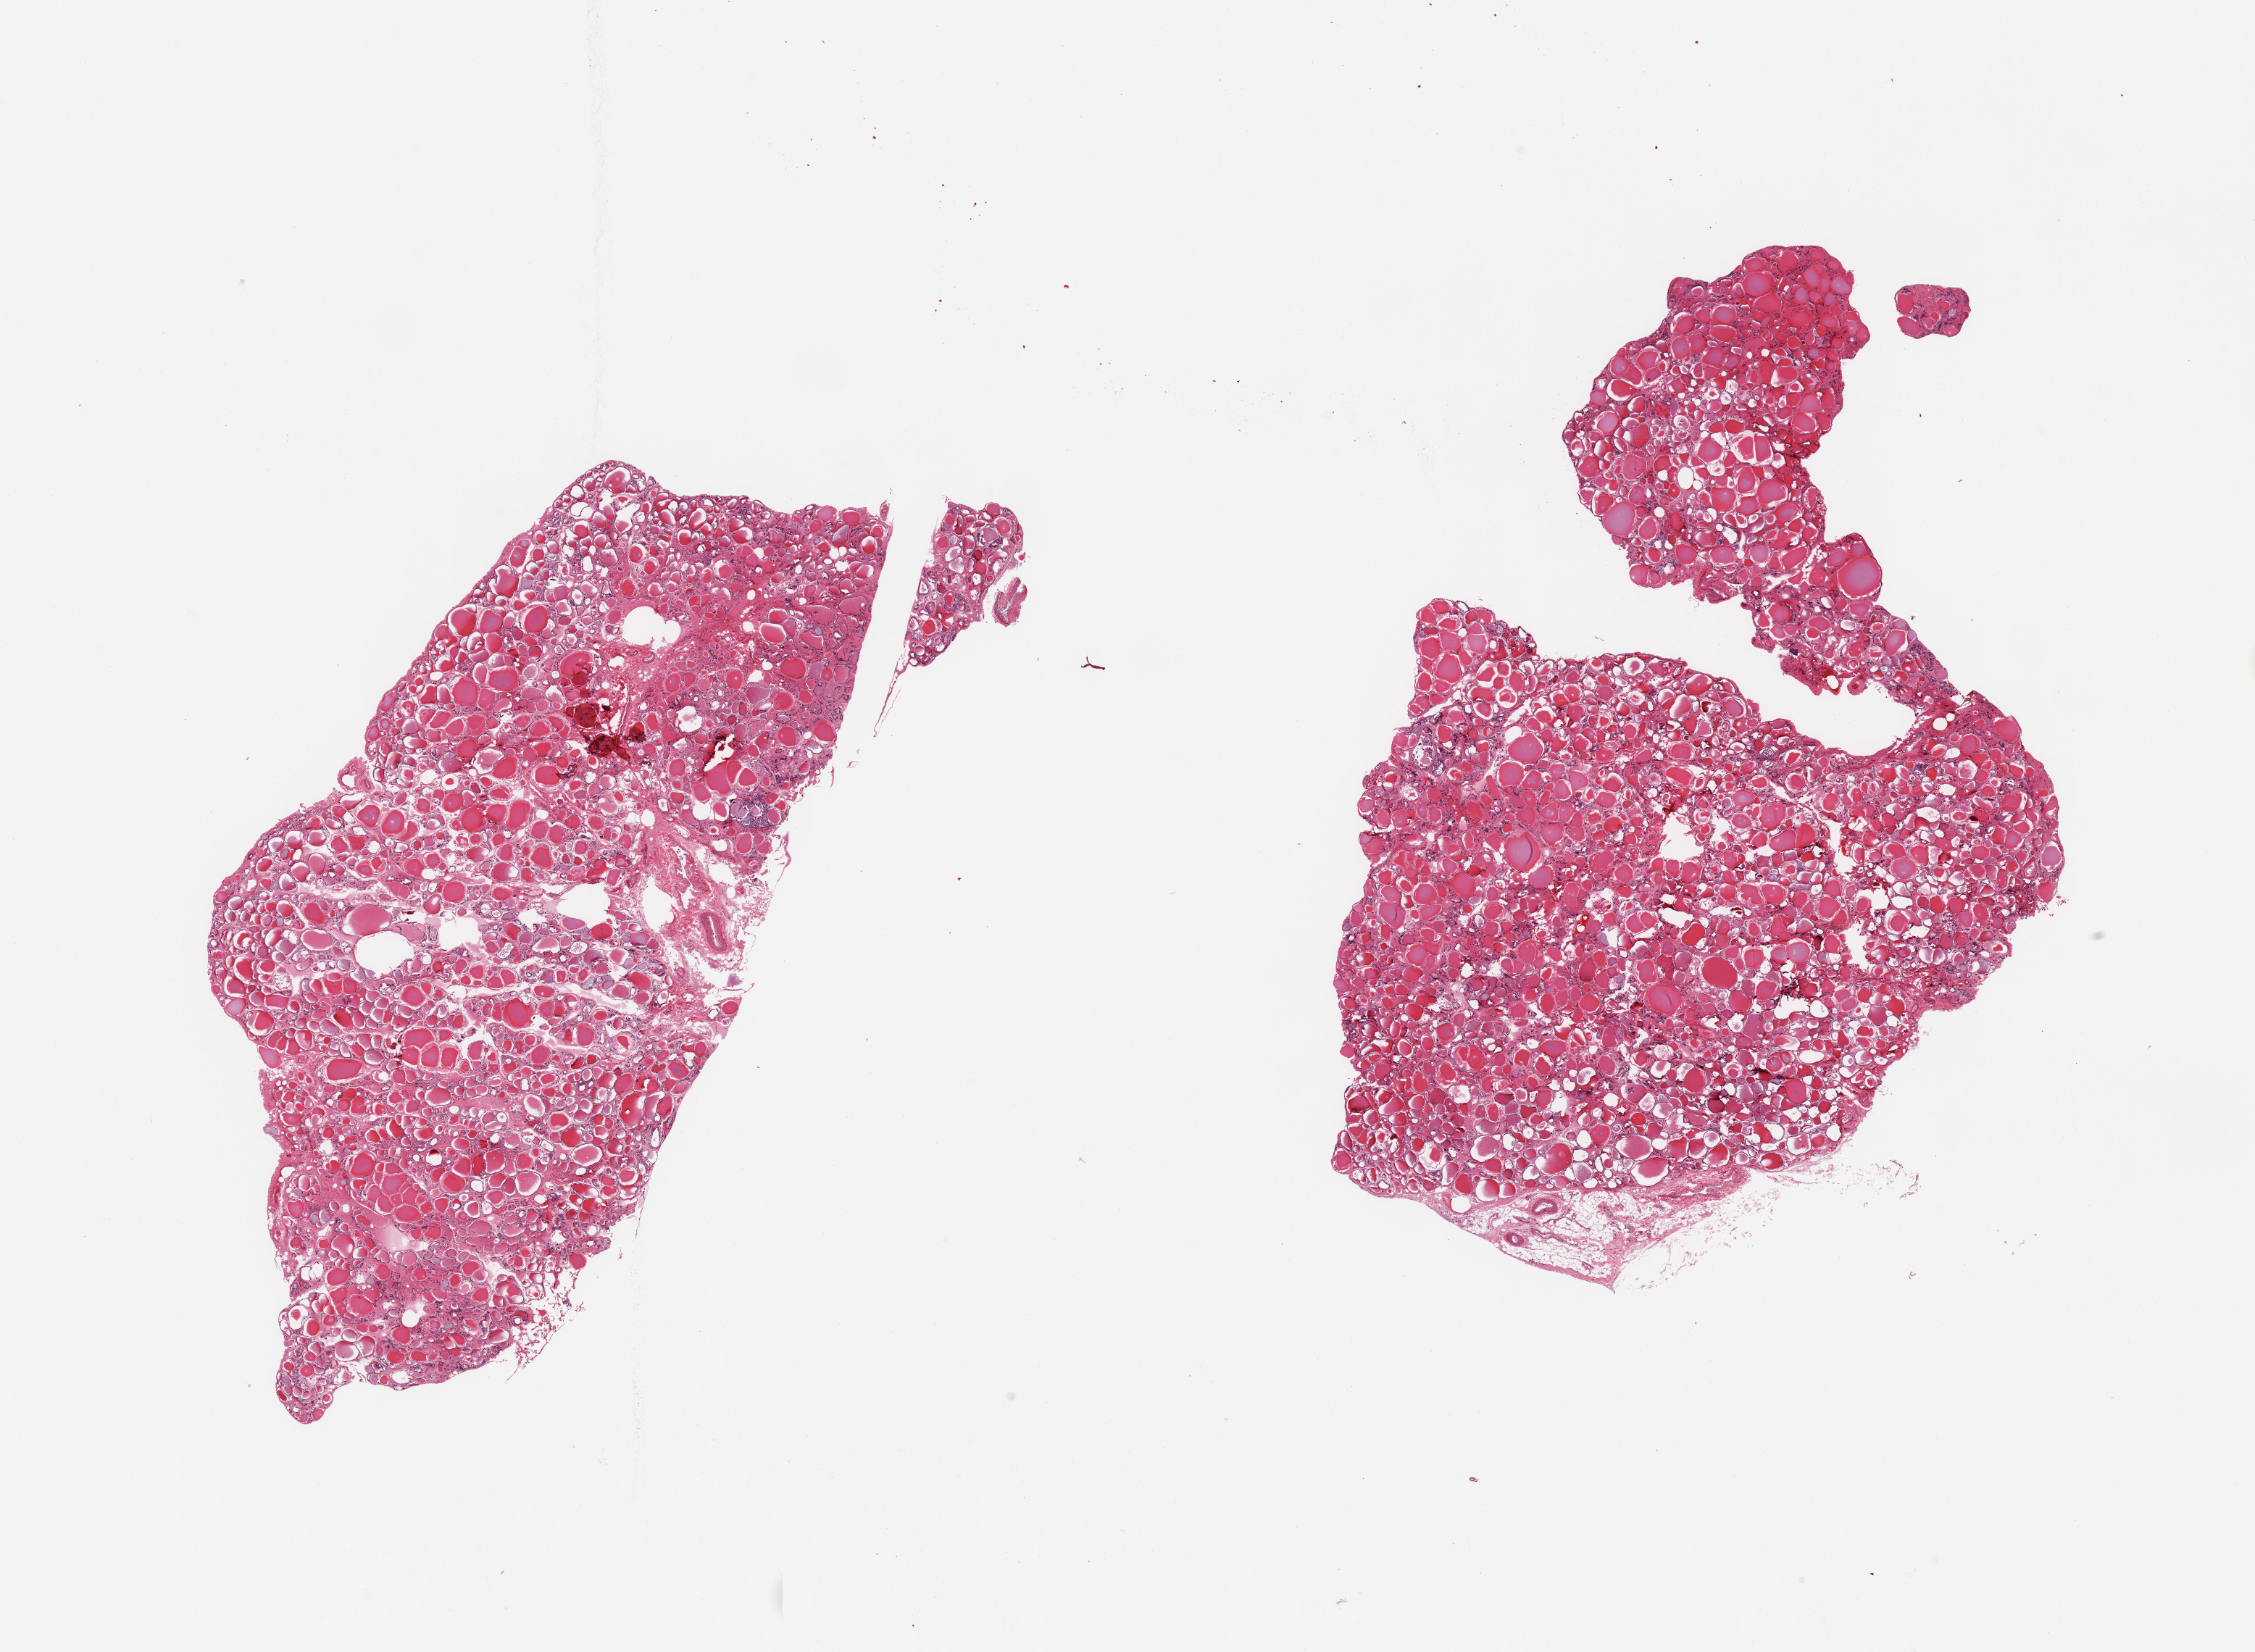
Digitized hematoxylin and eosin (H&E)-stained section, a low-resolution overview of the entire scanned area, about 24.6 x 18.0 mm (slide scanned at 20x), PAXgene-fixed paraffin-embedded (PFPE) section, sampled site (target tissue): thyroid, tissue donor sample. Female donor.
Reviewer comment on this tissue sample: 2 pieces, no abnormalities.